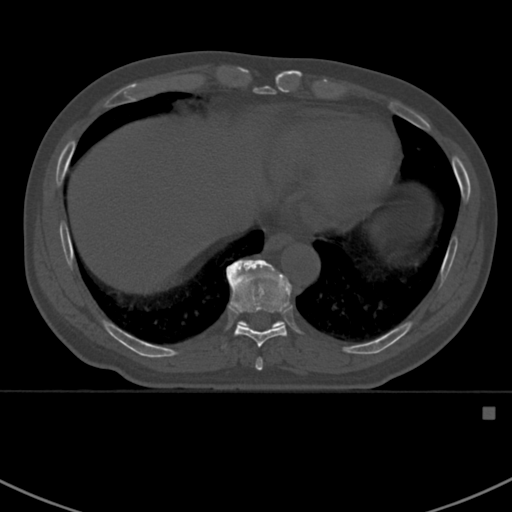
CT including the spine, one axial slice; position 380 of 412 along the scan axis; 120 kVp; bone window (W 1800 / L 400 HU); 1.5 mm slice thickness; 512 × 512 image matrix, field of view 358 × 358 mm. Male patient, age 59 years. Case-level facts recorded for this patient, not image findings: primary cancer: prostate.
Annotated regions visible in this slice (semi-automatic segmentation, software-assisted and operator-edited):
- T10 vertebra: bounding box [x1, y1, x2, y2] px = [226, 259, 284, 328]
- T8 vertebra: [255, 358, 263, 371]
- T9 vertebra: [227, 260, 292, 348]